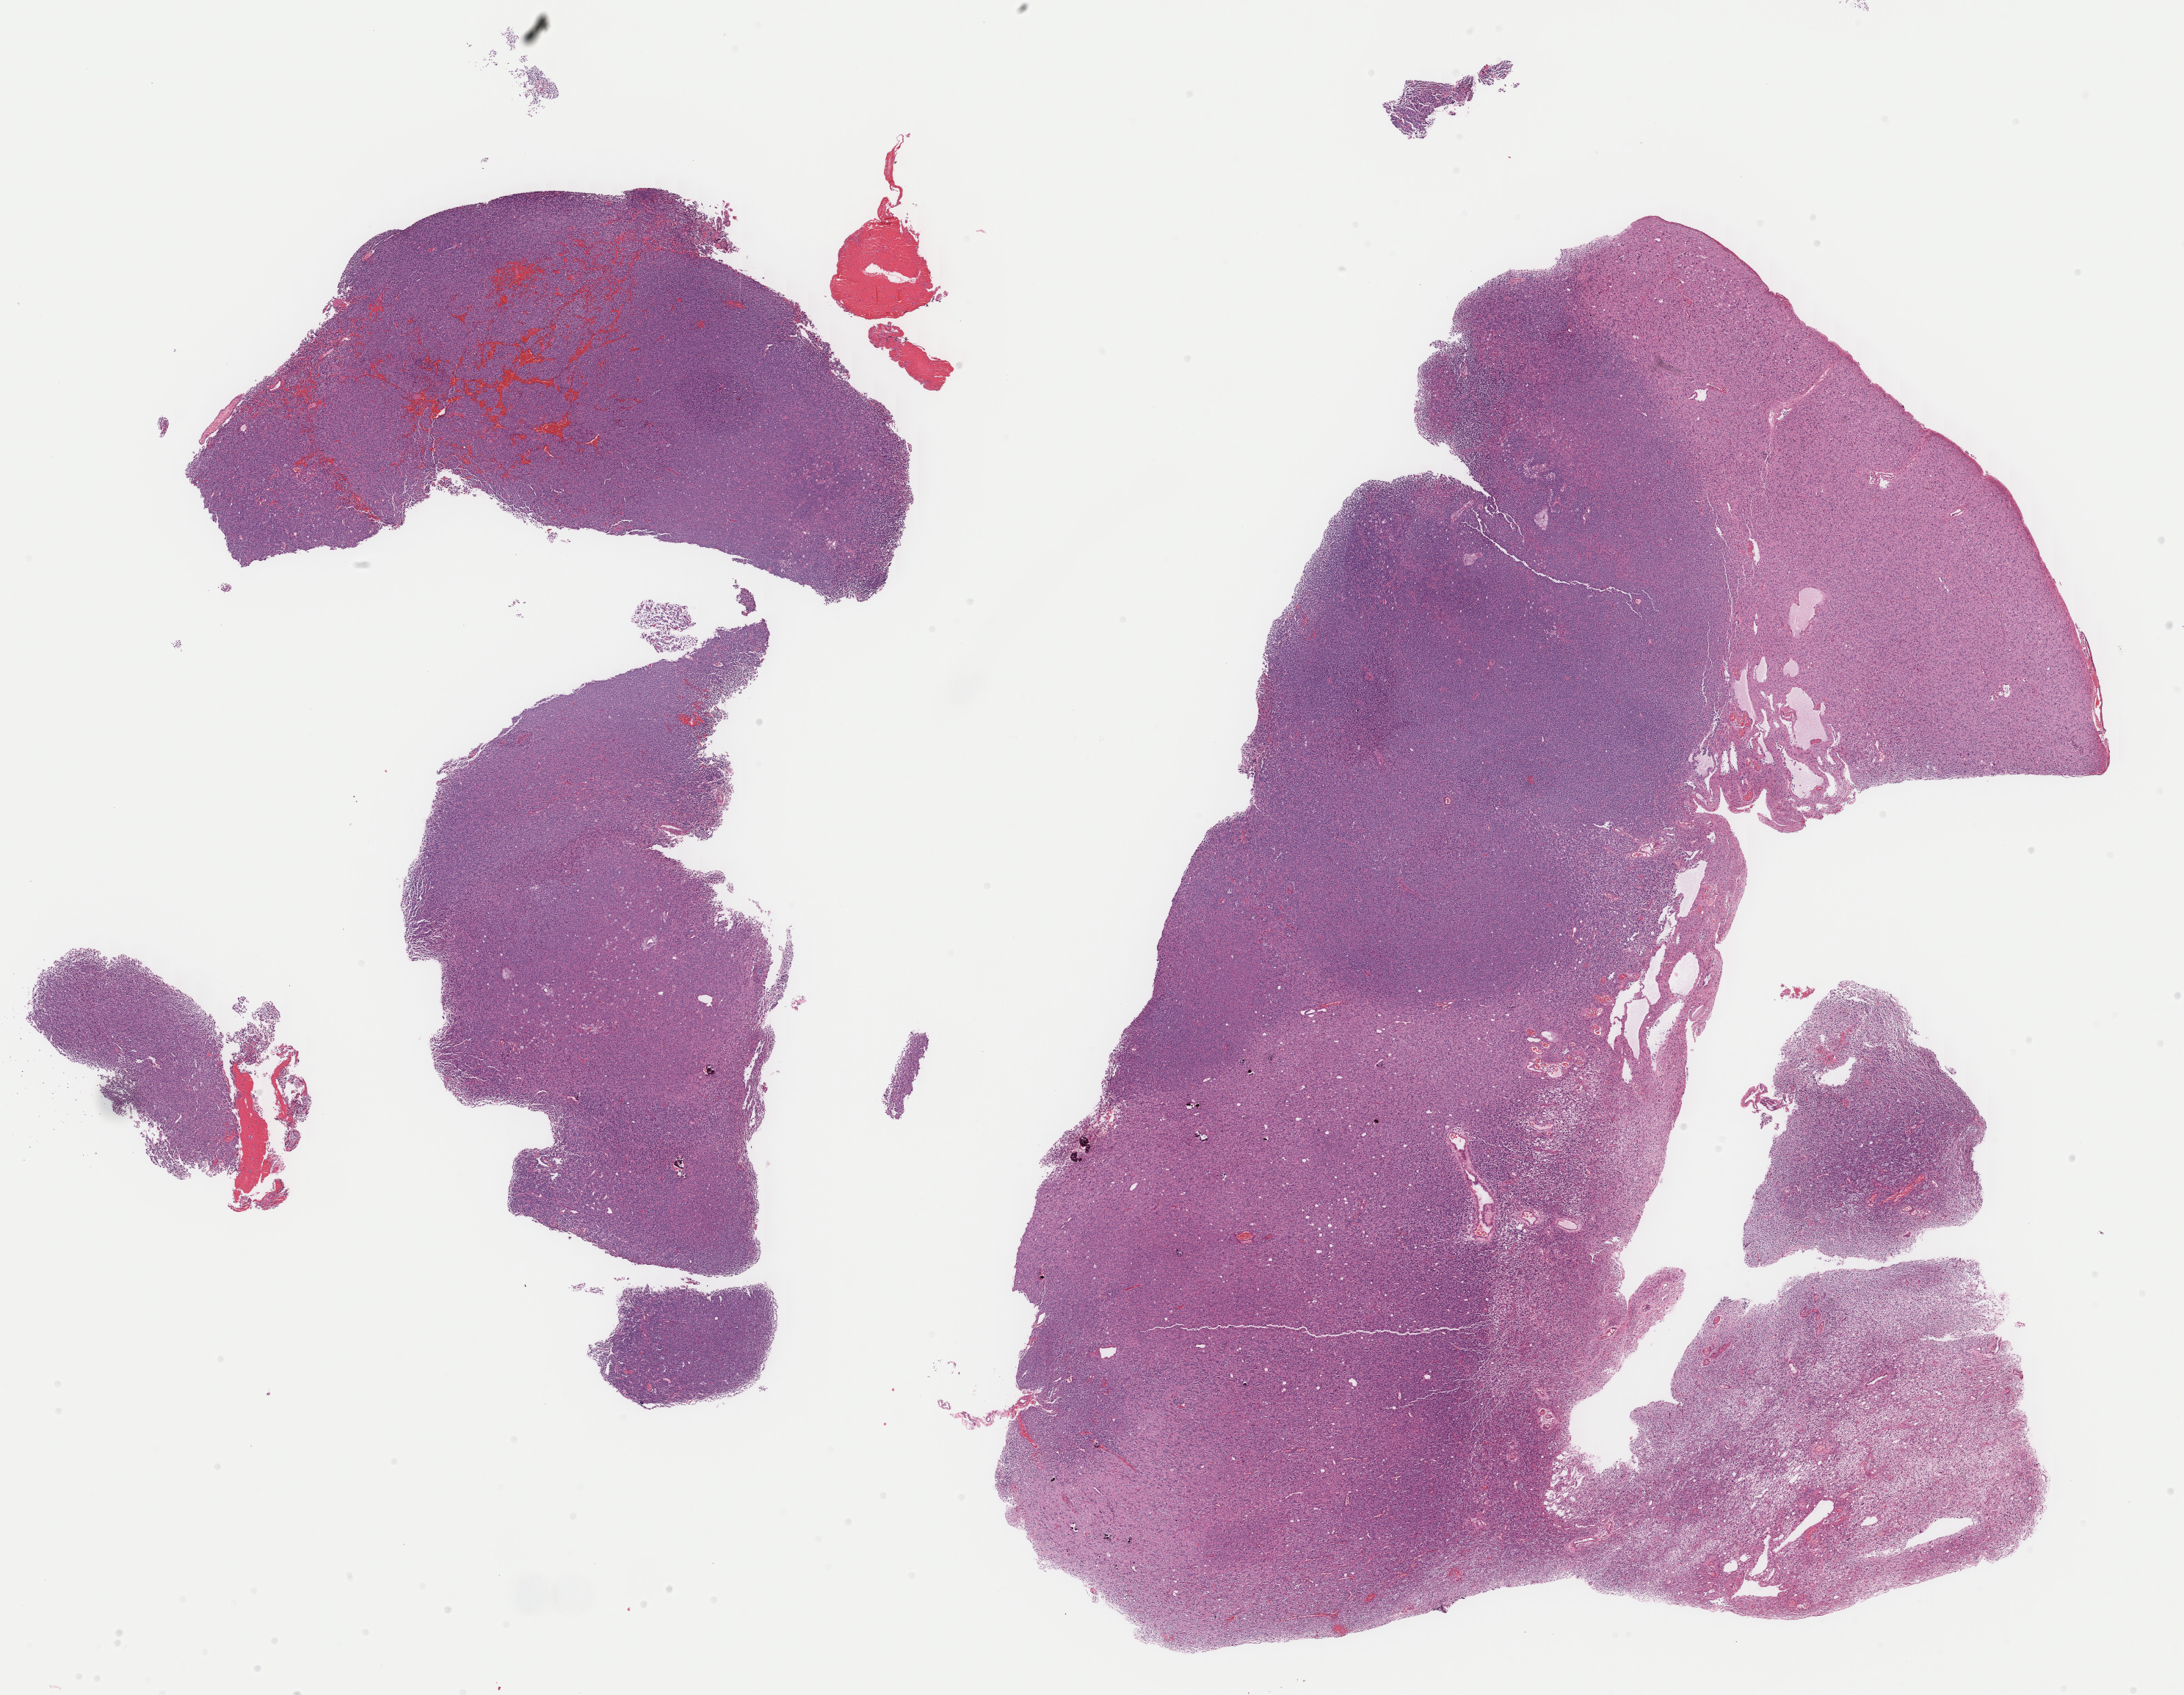
Whole-slide histology image, H&E, a low-resolution overview of the entire scanned area, about 23.4 x 18.2 mm (acquisition: 40x scan), formalin-fixed paraffin-embedded (FFPE) diagnostic section, primary tumour sample from the brain. Patient: male, age at initial diagnosis 34 years. Histologic grade: G3 (poorly differentiated).
Histologic diagnosis: Oligodendroglioma, anaplastic (frontal lobe).